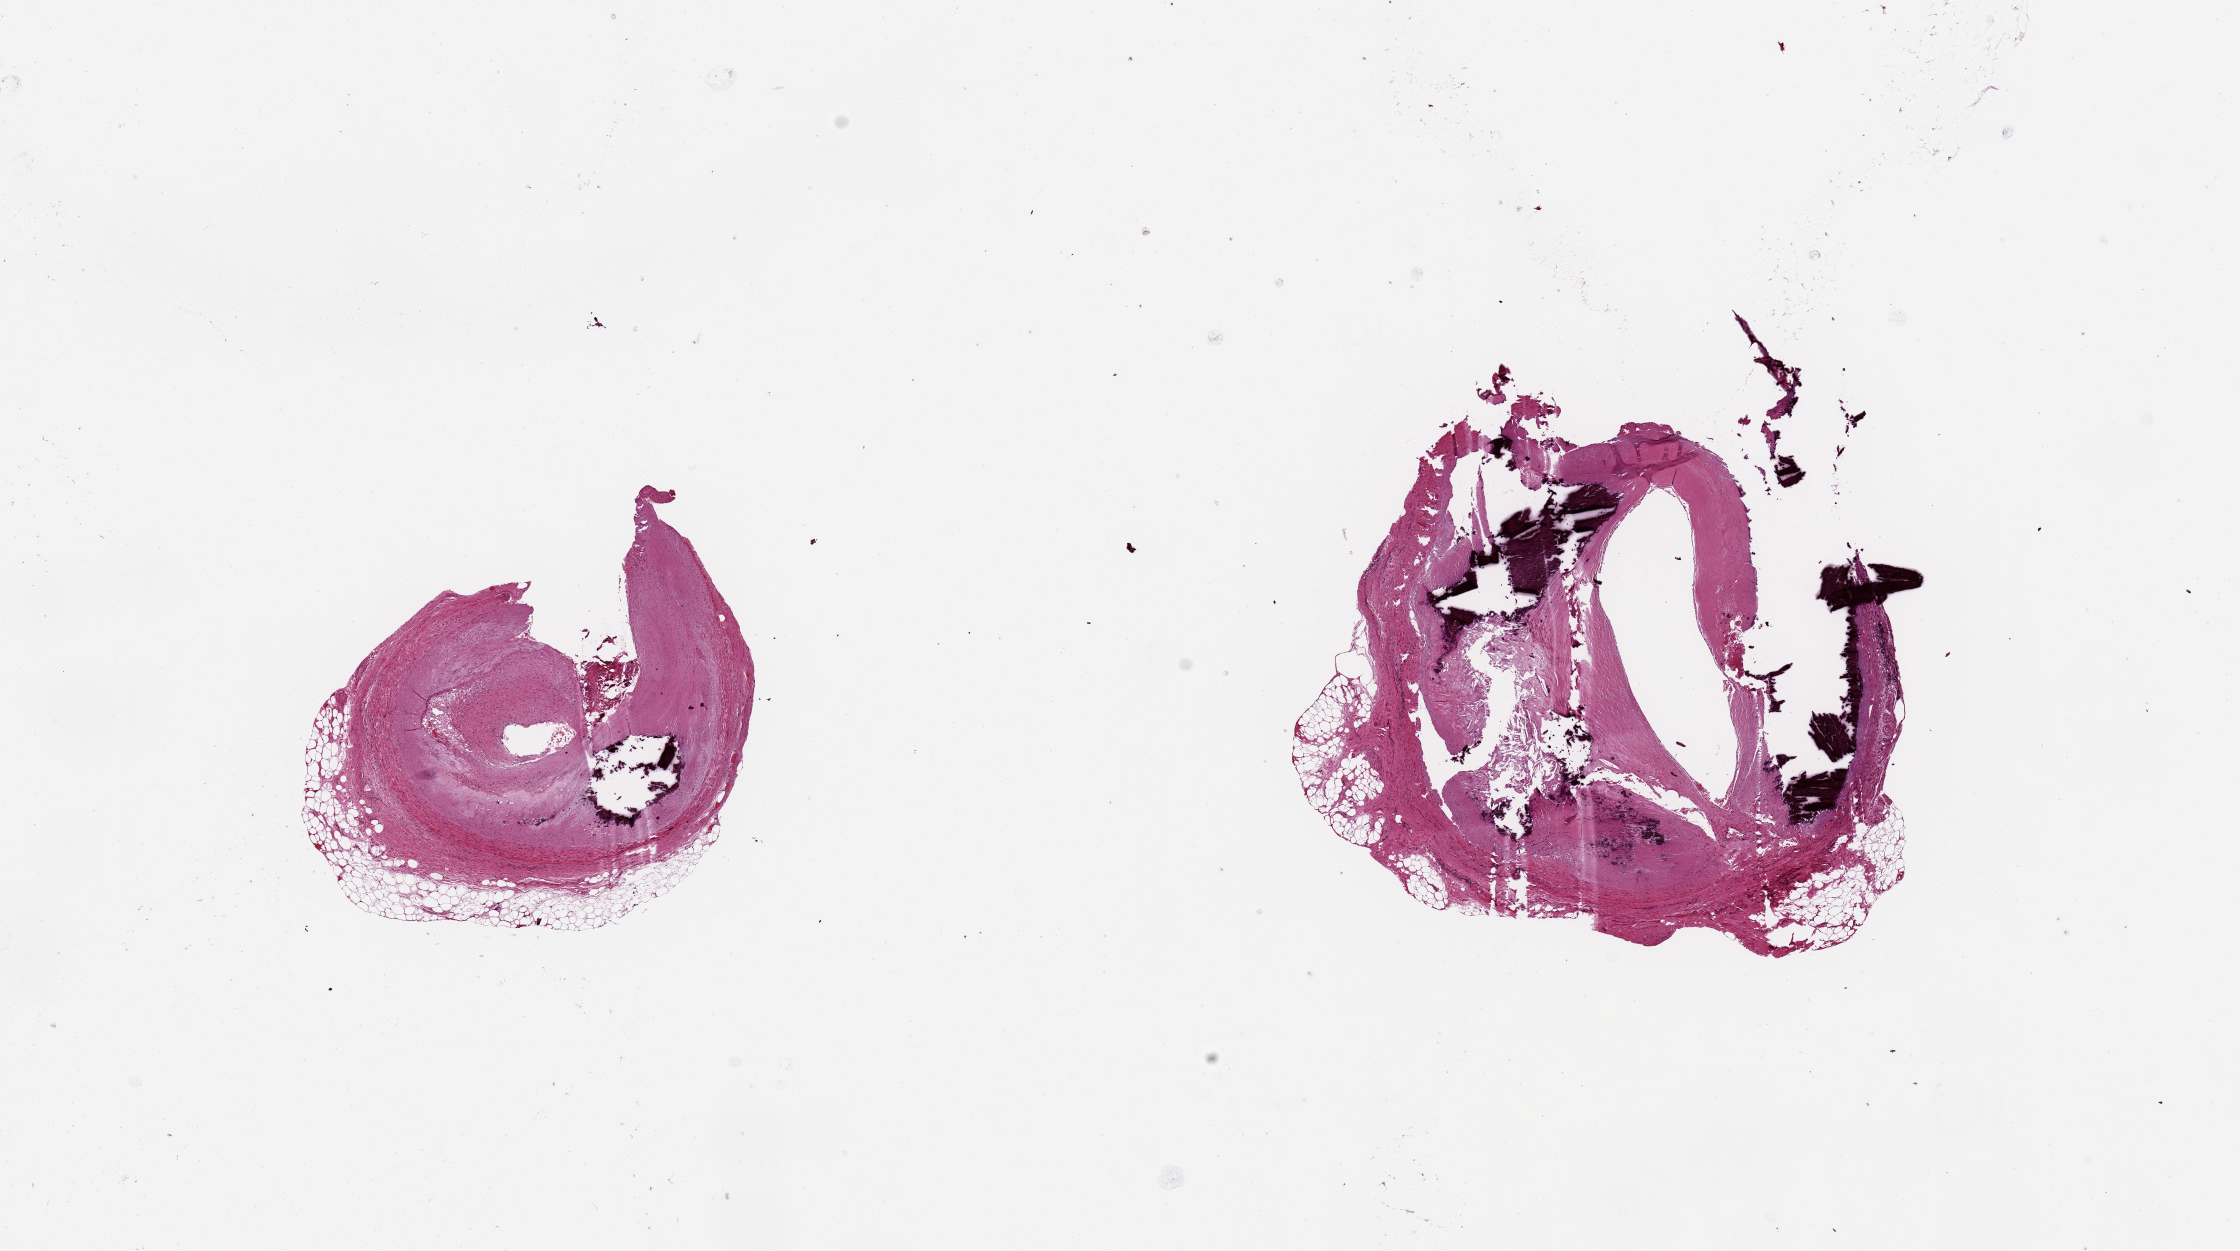
Whole-slide image, hematoxylin and eosin (H&E) stain, a low-resolution overview of the entire scanned area, about 17.7 x 9.9 mm (from a 20x scan), PAXgene-fixed, paraffin-embedded tissue, target tissue: coronary artery, donor tissue sample. Donor sex: male.
Reviewer comment on this tissue sample: 2 pieces ~3.5mm d, severely calcified, atherosclerotic, subtotally occluded, aliquots are shattered.